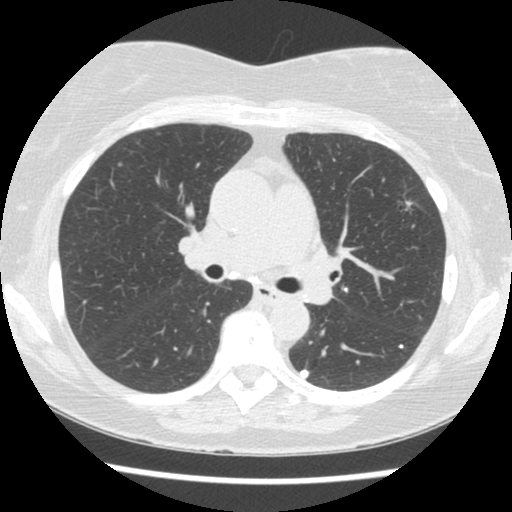
Low-dose screening chest CT, one axial slice; reconstruction kernel STANDARD; 120 kVp; lung window (W 1500 / L -600 HU); 512 × 512 image matrix, field of view 310 × 310 mm.
Outlined on this slice (outlined manually by an expert reader):
- lesion 1 (tumor, upper lobe of left lung): bounding box (x1, y1, x2, y2) in pixels: (405, 201, 413, 211)